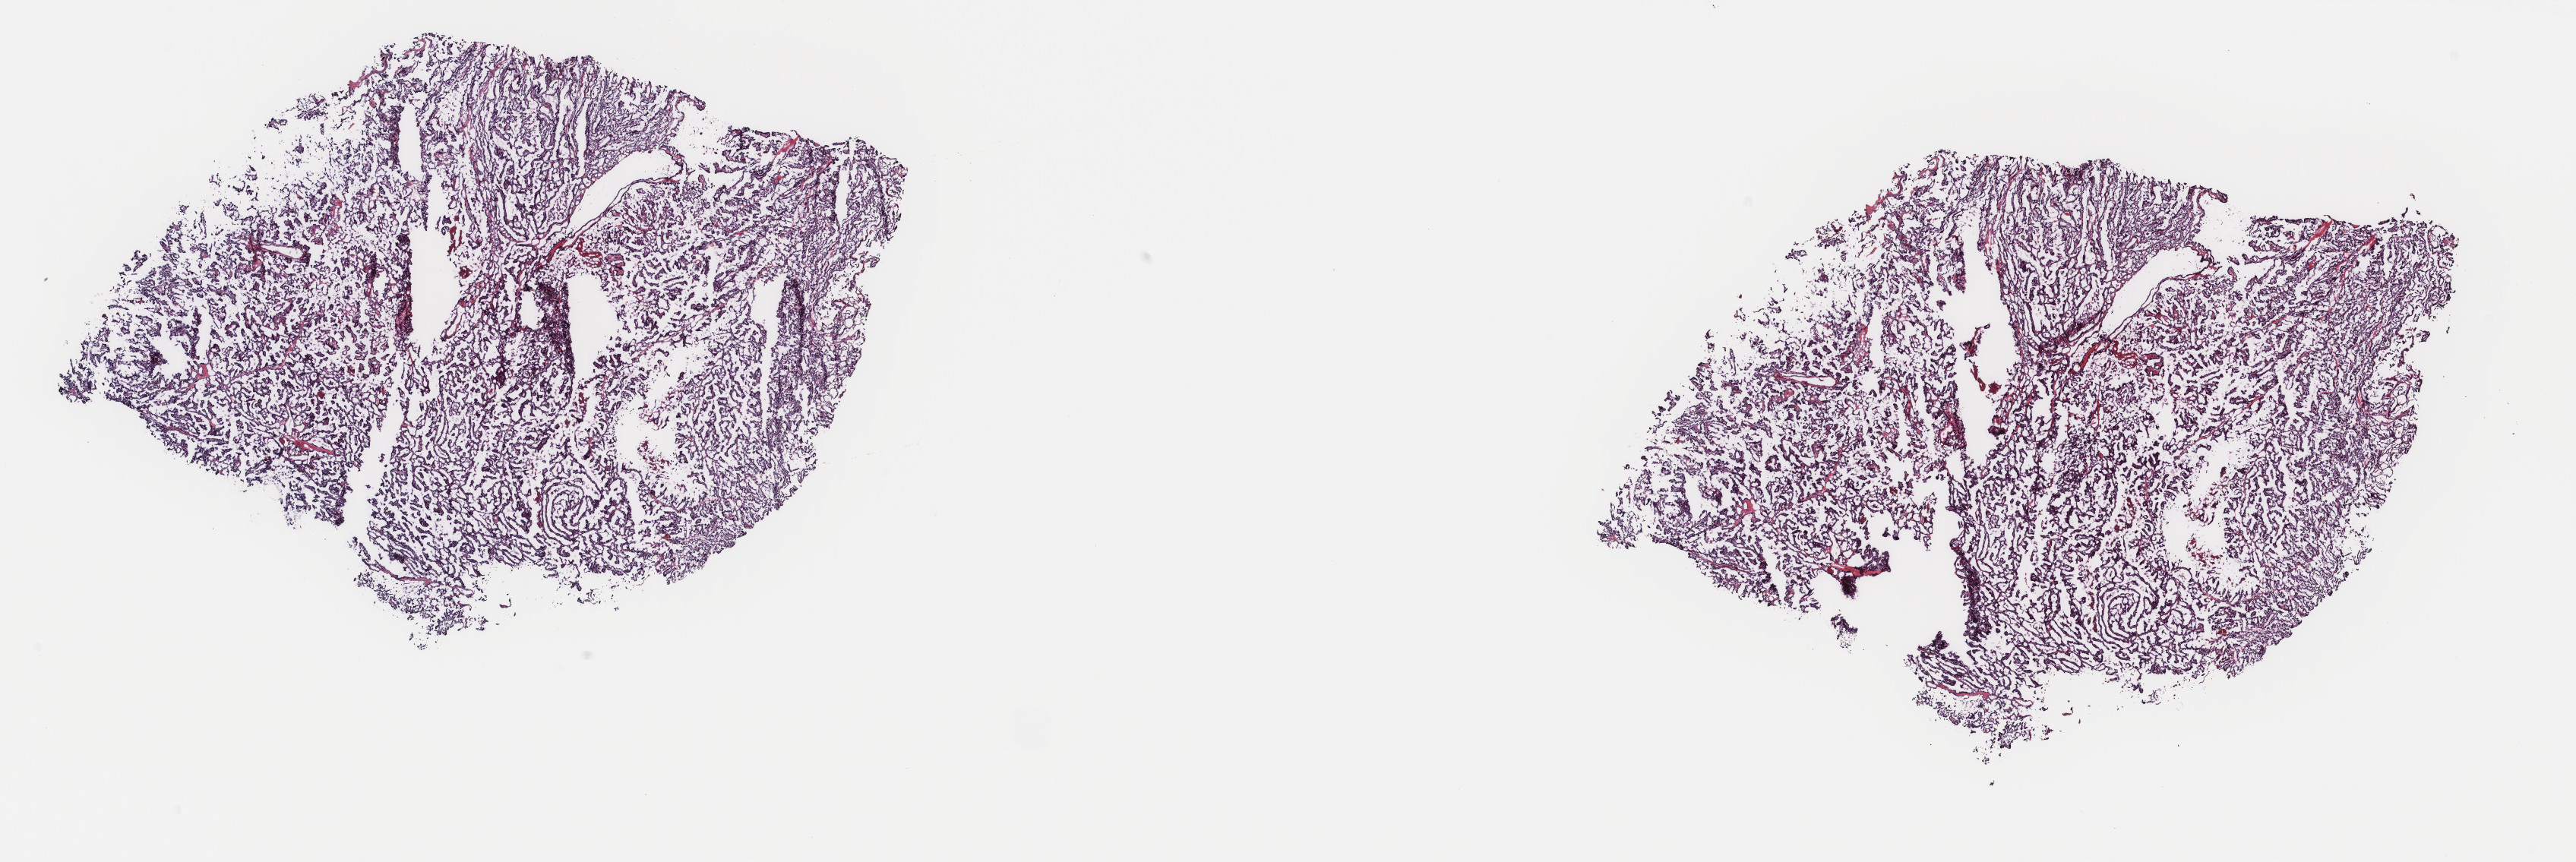
H&E-stained whole-slide image, shown as a low-resolution overview of the whole scanned area (about 26.9 x 9.0 mm, slide scanned at 40x). Frozen section from the top of the tissue portion. Sample: primary tumour, thyroid. Female patient; age at initial diagnosis 28 years. Slide review estimates, as recorded: tumour cells 100%, tumour nuclei 95%, normal cells 0%, stromal cells 0%, necrosis 0%. Inflammatory infiltration, as recorded: lymphocyte infiltration 0%, monocyte infiltration 0%, neutrophil infiltration 0%.
- laterality: left
- histologic diagnosis: Papillary adenocarcinoma, NOS (thyroid gland)
- TNM: T2 N1 M0
- AJCC pathologic stage: I